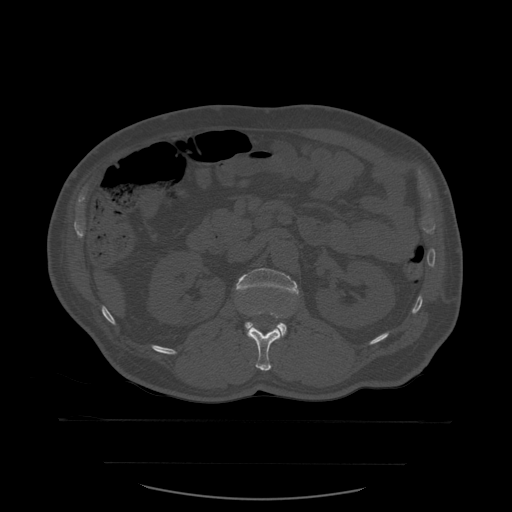
CT including the spine, one axial slice. Slice 235 of 590 in the series (ordered by position). Bone window (W 1800 / L 400 HU). 1.25 mm slice thickness. 512 × 512 image matrix. Patient age 71 years. Case-level facts recorded for this patient, not image findings: primary cancer: lung; vertebrae with lytic lesions (as recorded): T1, T2, L5, S1.
Outlined on this slice (semi-automatic segmentation, software-assisted and operator-edited):
- L1 vertebra: bounding box (x1, y1, x2, y2) in pixels: (242, 309, 282, 371)
- L2 vertebra: (236, 269, 299, 337)